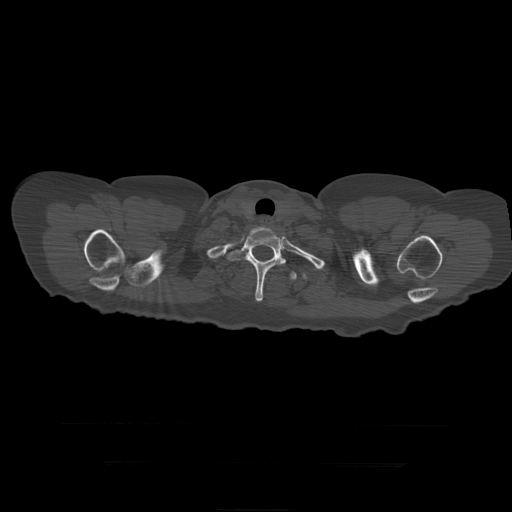
CT including the spine, one axial slice; slice 377 of 399 in the series (ordered by position); 120 kVp; bone window (W 1800 / L 400 HU); 1.25 mm slice thickness; 512 × 512 image matrix. Patient age 41 years. Case-level facts recorded for this patient, not image findings: primary cancer: breast.
Outlined on this slice (semi-automatic segmentation, software-assisted and operator-edited):
- T1 vertebra: box from (x=249, y=226) to (x=276, y=237) px
- T2 vertebra: (x=227, y=232)–(x=286, y=302)
- T3 vertebra: (x=290, y=272)–(x=297, y=280)